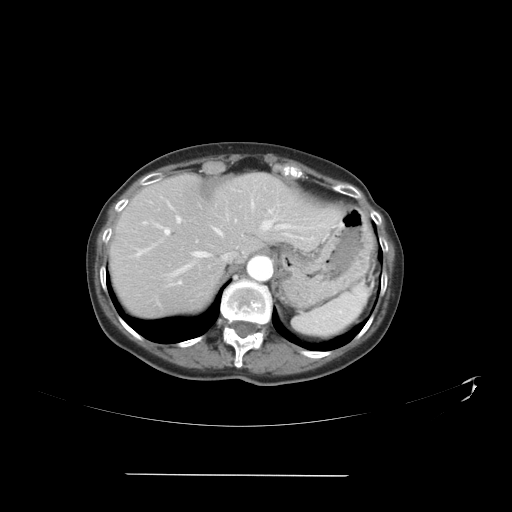
Contrast-enhanced abdominal CT, one axial slice; slice 30 of 41 in the series (ordered by position); intravenous contrast given; soft-tissue window (W 400 / L 40 HU); 512 × 512 image matrix, field of view 431 × 431 mm. Female patient, age 74 years. From the clinical record (not read from this slice): diagnosis: colorectal cancer liver metastases, imaged before liver resection; multiple liver metastases: yes; largest metastasis: 3.3 cm; chemotherapy before resection: yes.
Annotated regions visible in this slice (outlined manually by an expert reader):
- hepatic veins: box from (x=150, y=192) to (x=290, y=276) px
- liver: (x=111, y=174)–(x=339, y=316)
- planned liver remnant (the part of the liver to remain after resection): (x=116, y=174)–(x=327, y=256)
- portal vein (with intrahepatic branches): (x=136, y=210)–(x=270, y=284)